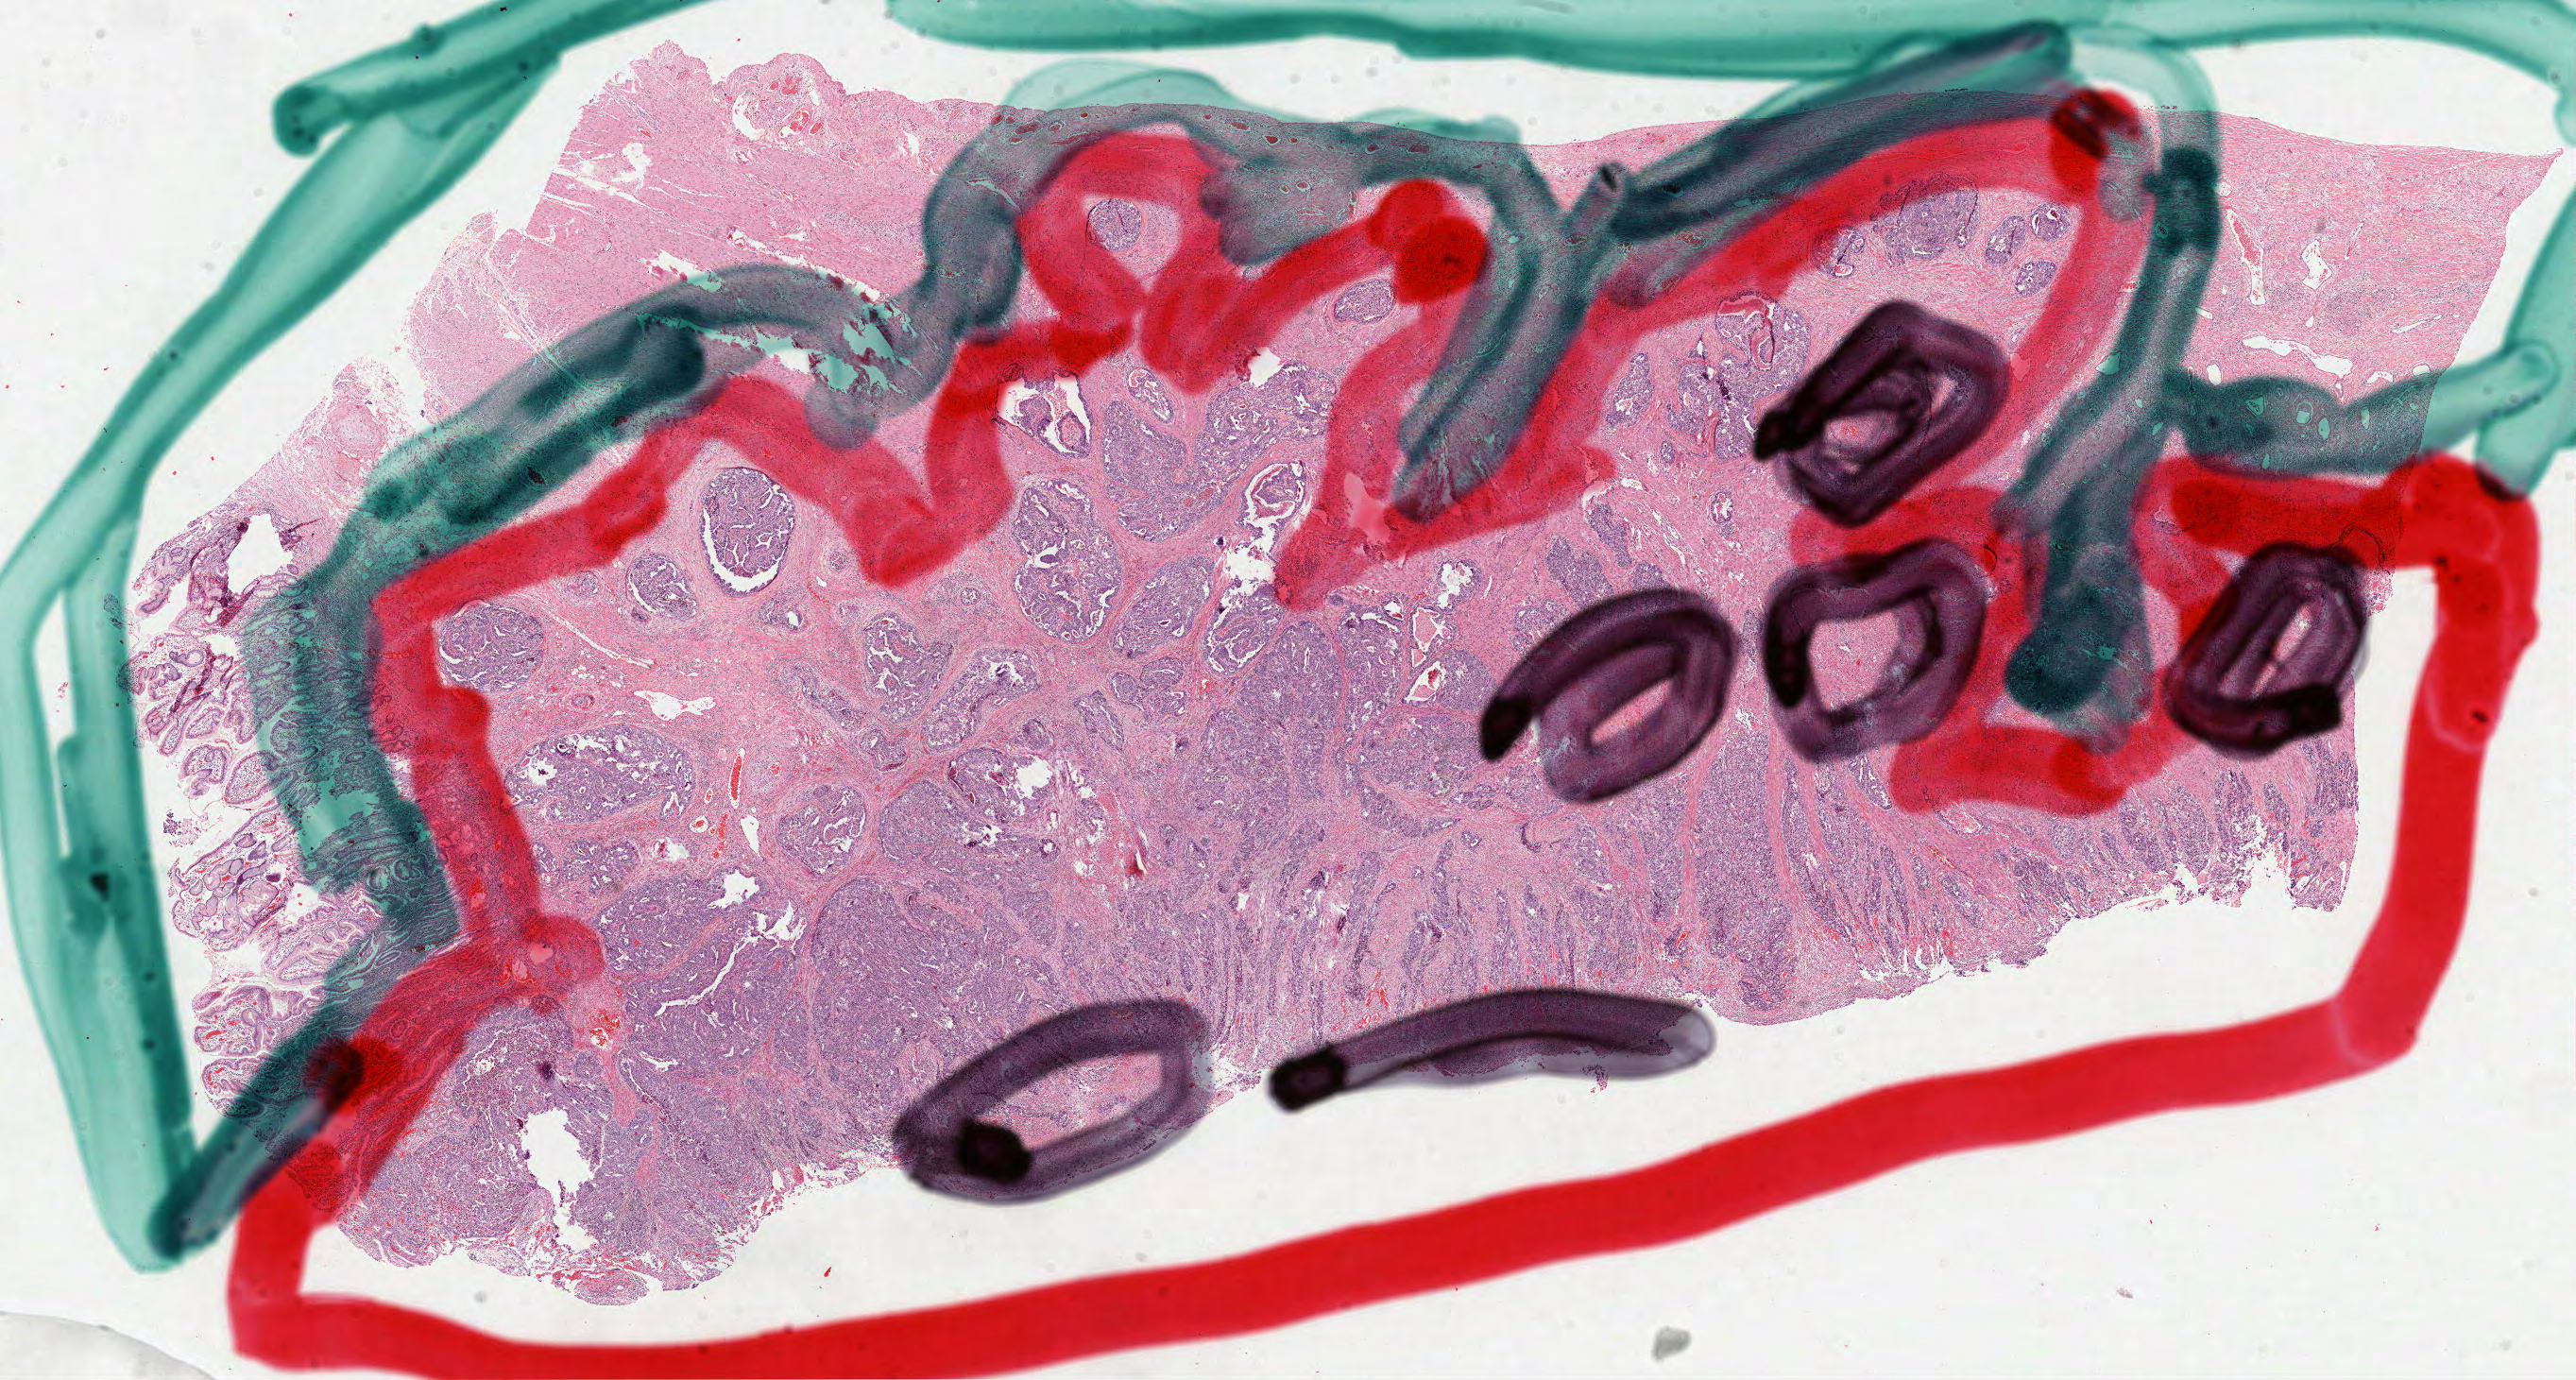
Hematoxylin and eosin (H&E) stained whole-slide image, a low-resolution overview of the entire scanned area, about 22.0 x 11.8 mm (slide scanned at 40x); FFPE section; primary tumour sample from the stomach. Male, age 65 years at initial diagnosis. Histologic grade: G2 (moderately differentiated).
- TNM: T3 N0 M0
- AJCC pathologic stage: IIA
- pathologic diagnosis: Adenocarcinoma, NOS (body of stomach)